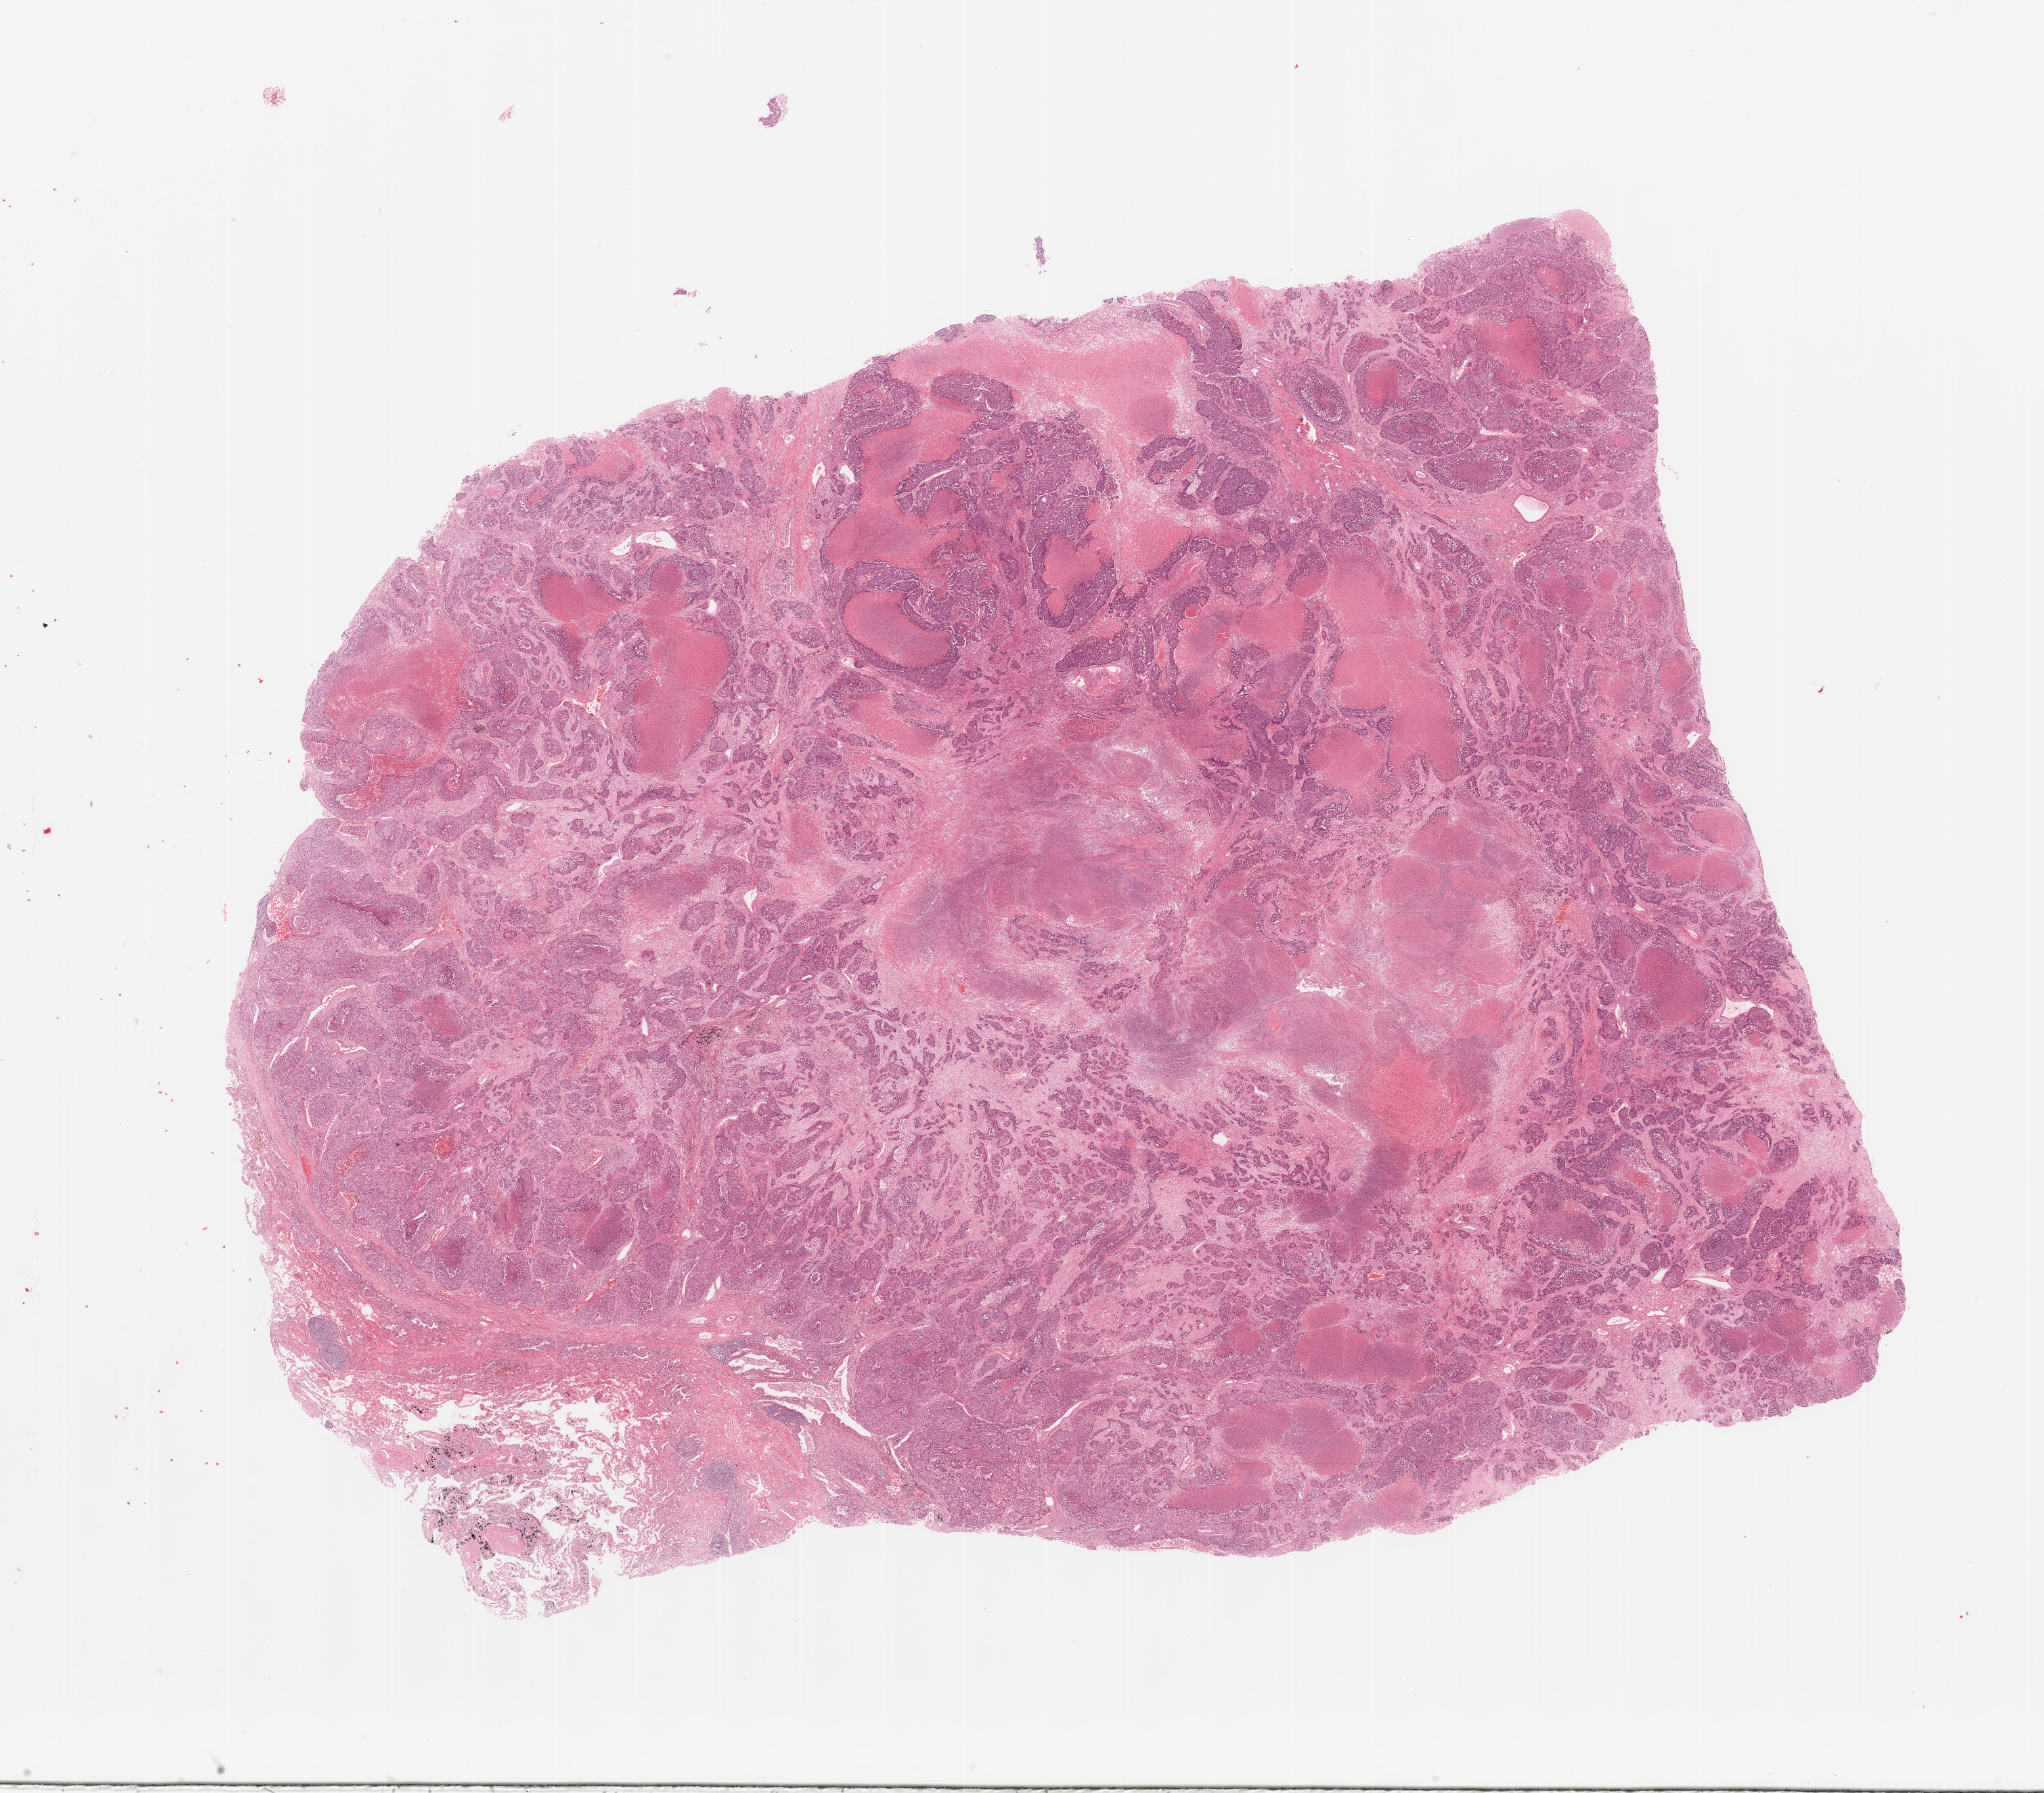
Digitized H&E-stained tissue section (whole slide), low-resolution overview of the scanned area, about 24.6 x 21.6 mm (slide scanned at 20x); tumour tissue sample, lung. Male, 58 y/o. Histologic grade: G3 (poorly differentiated).
Histologic diagnosis: Adenocarcinoma, NOS. AJCC pathologic stage: IB.